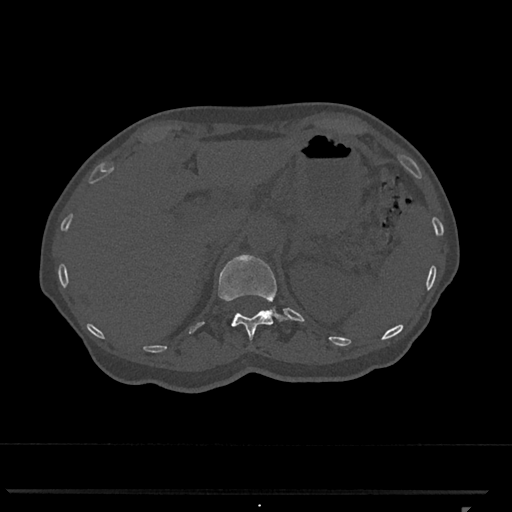
CT including the spine, one axial slice. Position 454 of 793 along the scan axis. Reconstruction kernel Br40s/3. 120 kVp. Bone window (W 1800 / L 400 HU). 0.5 mm slice thickness. 512 × 512 image matrix, field of view 380 × 380 mm. Female patient, age 62 years. From the clinical record (not read from this slice): primary cancer: renal.
Structures marked on this image (semi-automatic segmentation, software-assisted and operator-edited):
- T12 vertebra: bounding box <218,255,287,341> (left, top, right, bottom; pixels)